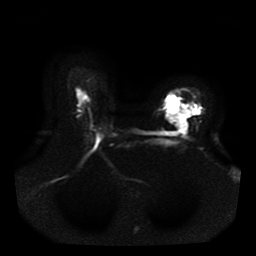
Breast MRI, one axial slice. Position 29 of 41 along the scan axis. Diffusion-weighted series; image 2 of 4 stored at this slice position (different b-values; order by instance number). 1.5 T. 5 mm slice thickness. 256 × 256 image matrix. Female patient.
Outlined on this slice (outlined manually by an expert reader):
- tumour on diffusion-weighted imaging: box from (x=166, y=96) to (x=201, y=132) px